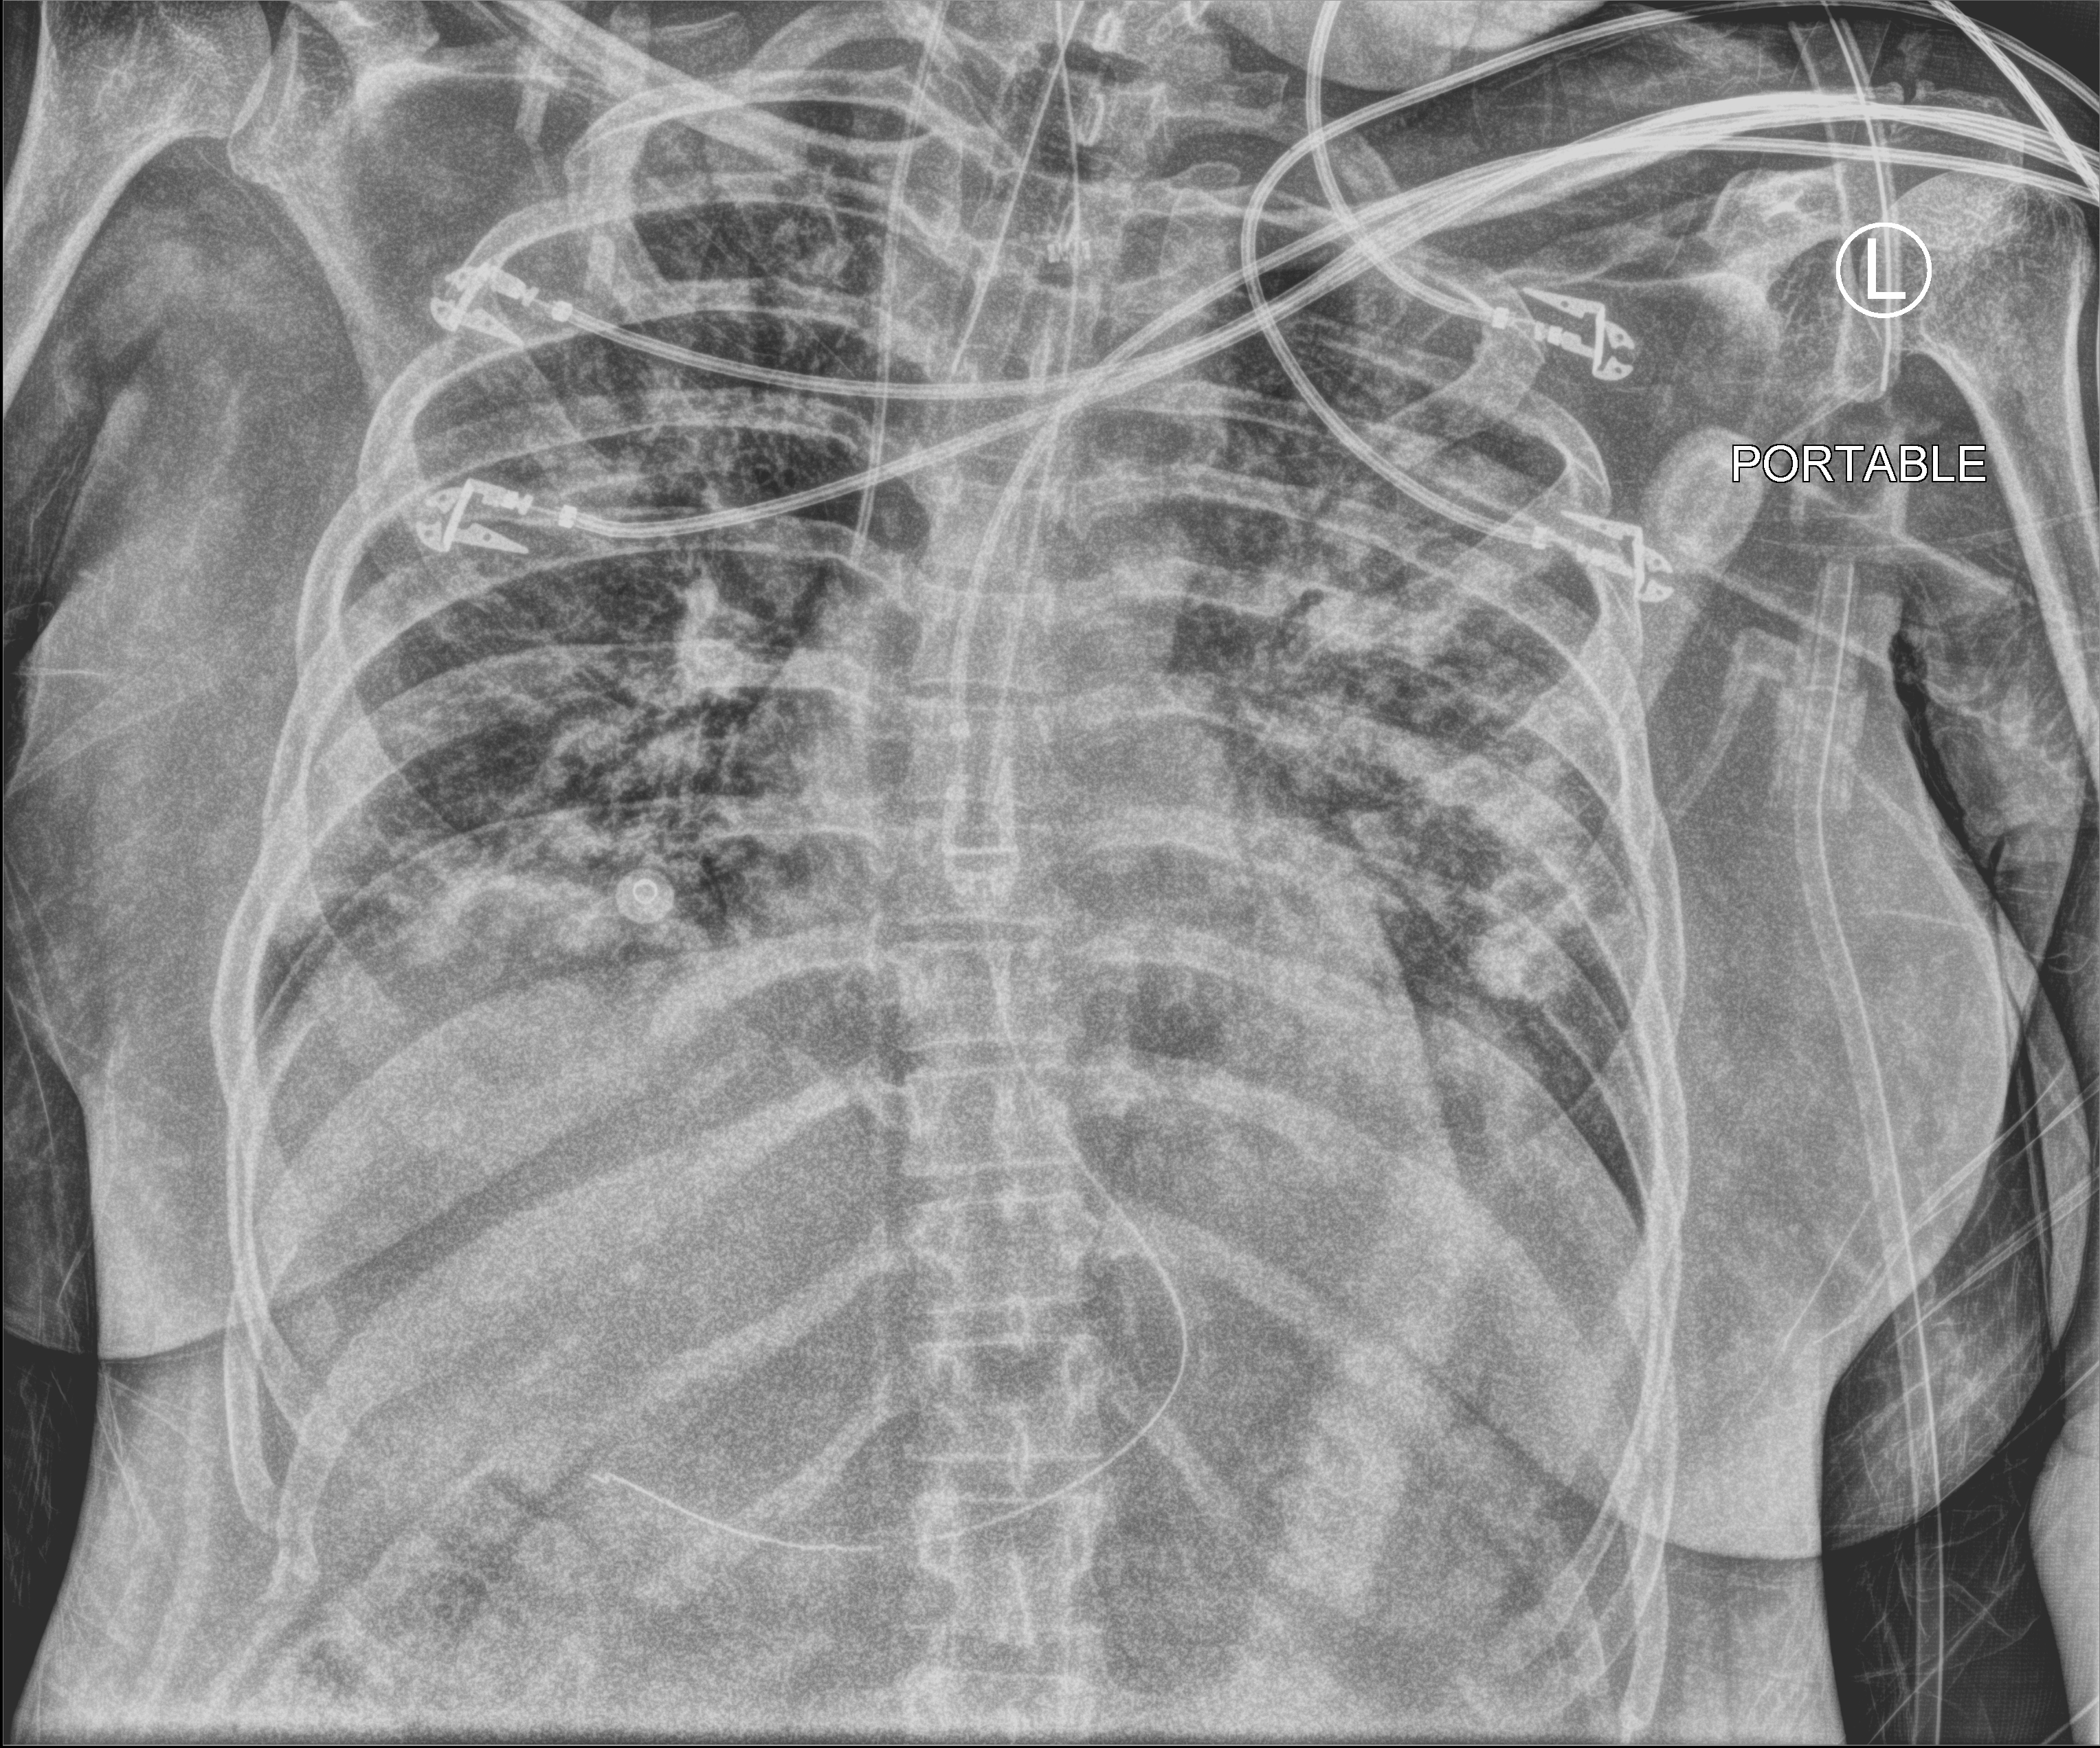
Portable chest radiograph. Adult patient hospitalised with COVID-19, age 18–59 years.
Hospital-stay facts (about this admission, not read from this image; timing relative to this image not recorded):
- admitted to intensive care during this hospital stay: yes
- other chronic lung disease (admission record): no
- mechanically ventilated during this hospital stay: yes